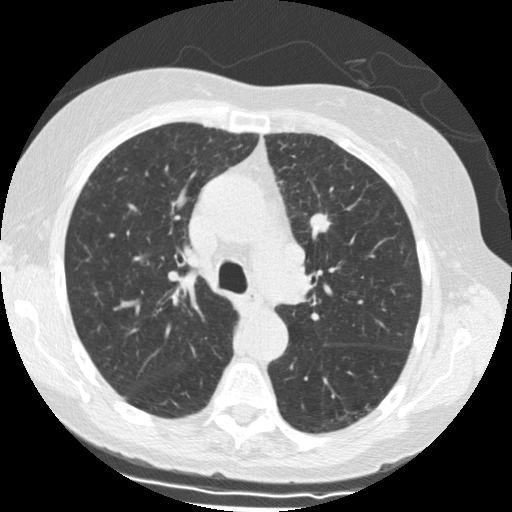
Axial slice from a low-dose chest CT screening exam, baseline screening round, lung window (W 1500 / L -600 HU), 2.5 mm slice thickness. Female, age 69 years at enrolment.
Lesion marked by an expert reader, bounding box (x1, y1, x2, y2) in pixels: (299, 205, 344, 245). The screening reader recorded 2 non-calcified nodules or masses ≥4 mm on this exam; which of them this box marks is not recorded. Official screen result: positive, change unspecified: nodule(s) >= 4 mm or enlarging nodule(s), mass(es), or other non-specific abnormalities suspicious for lung cancer. Participant outcome: lung cancer diagnosed 18 days after this screen — squamous cell carcinoma, NOS, left upper lobe, stage IIIA (AJCC 6th edition), 15 mm at pathology.